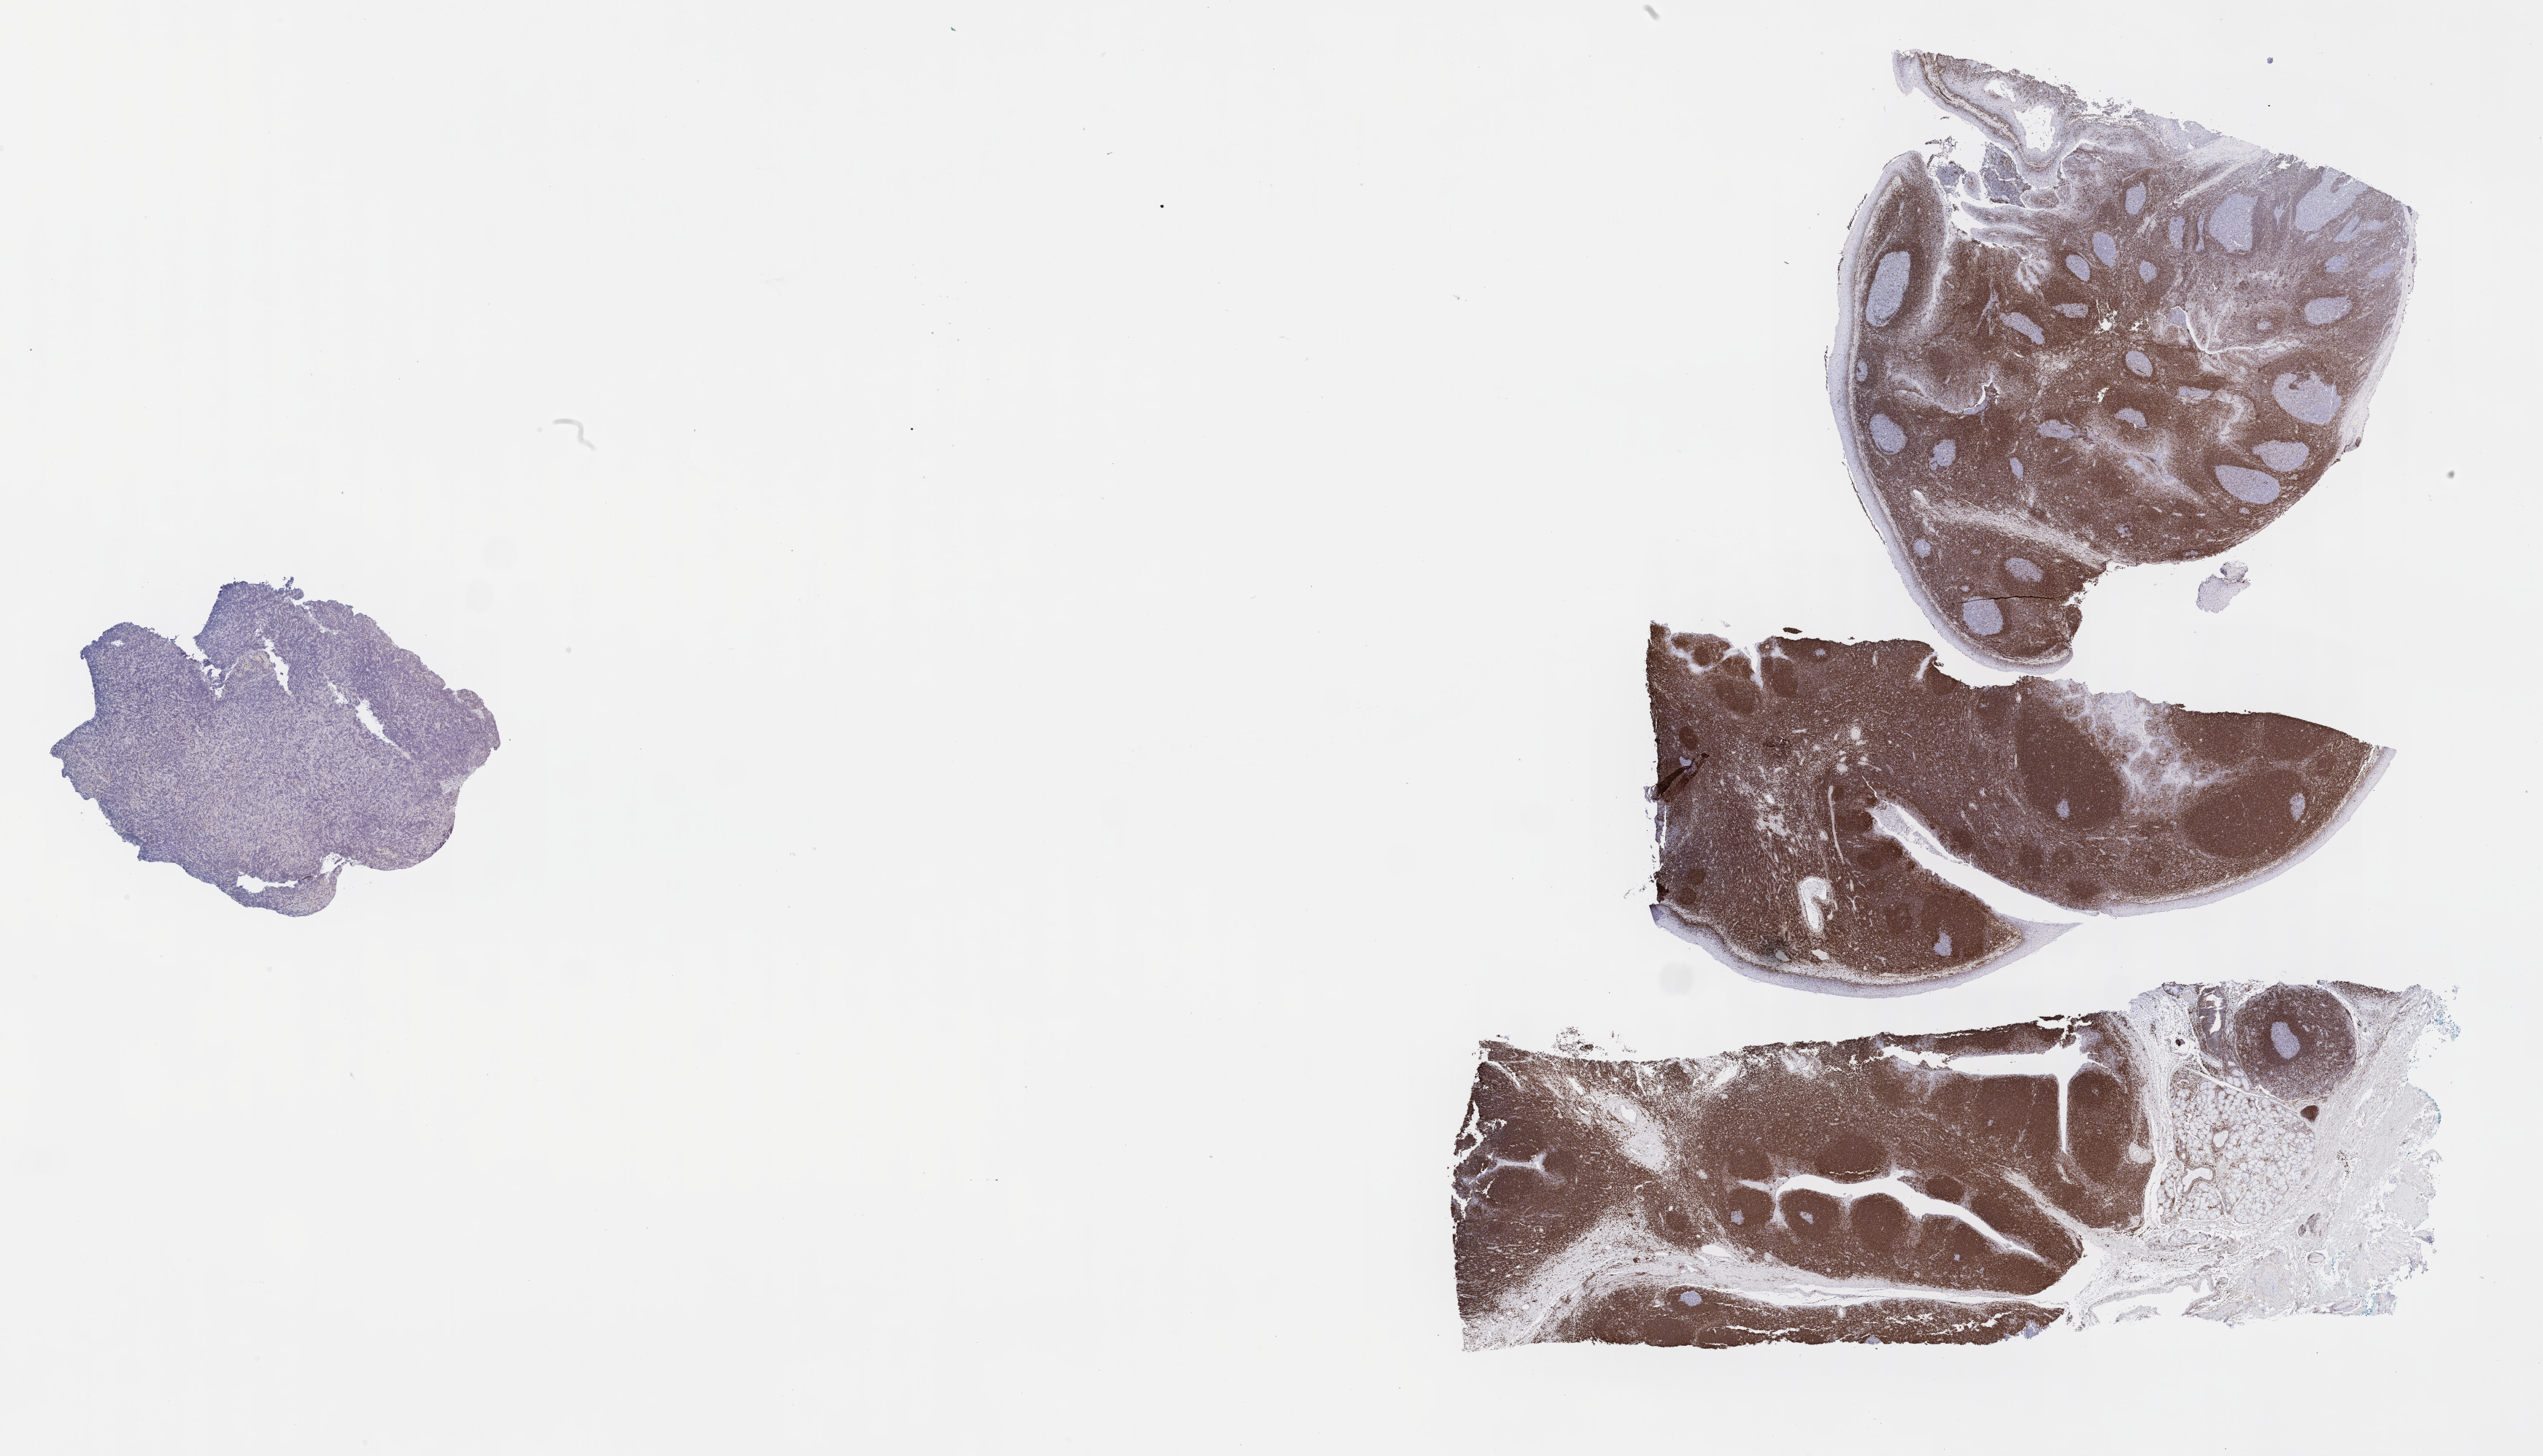
IHC for BCL2, whole-slide image — shown as a low-resolution overview of the whole scanned area (about 28.2 x 16.1 mm). Tumor tissue. Anatomic site: mandible. Male patient; age at initial diagnosis 8 years.
Diagnosis: Burkitt lymphoma, NOS.